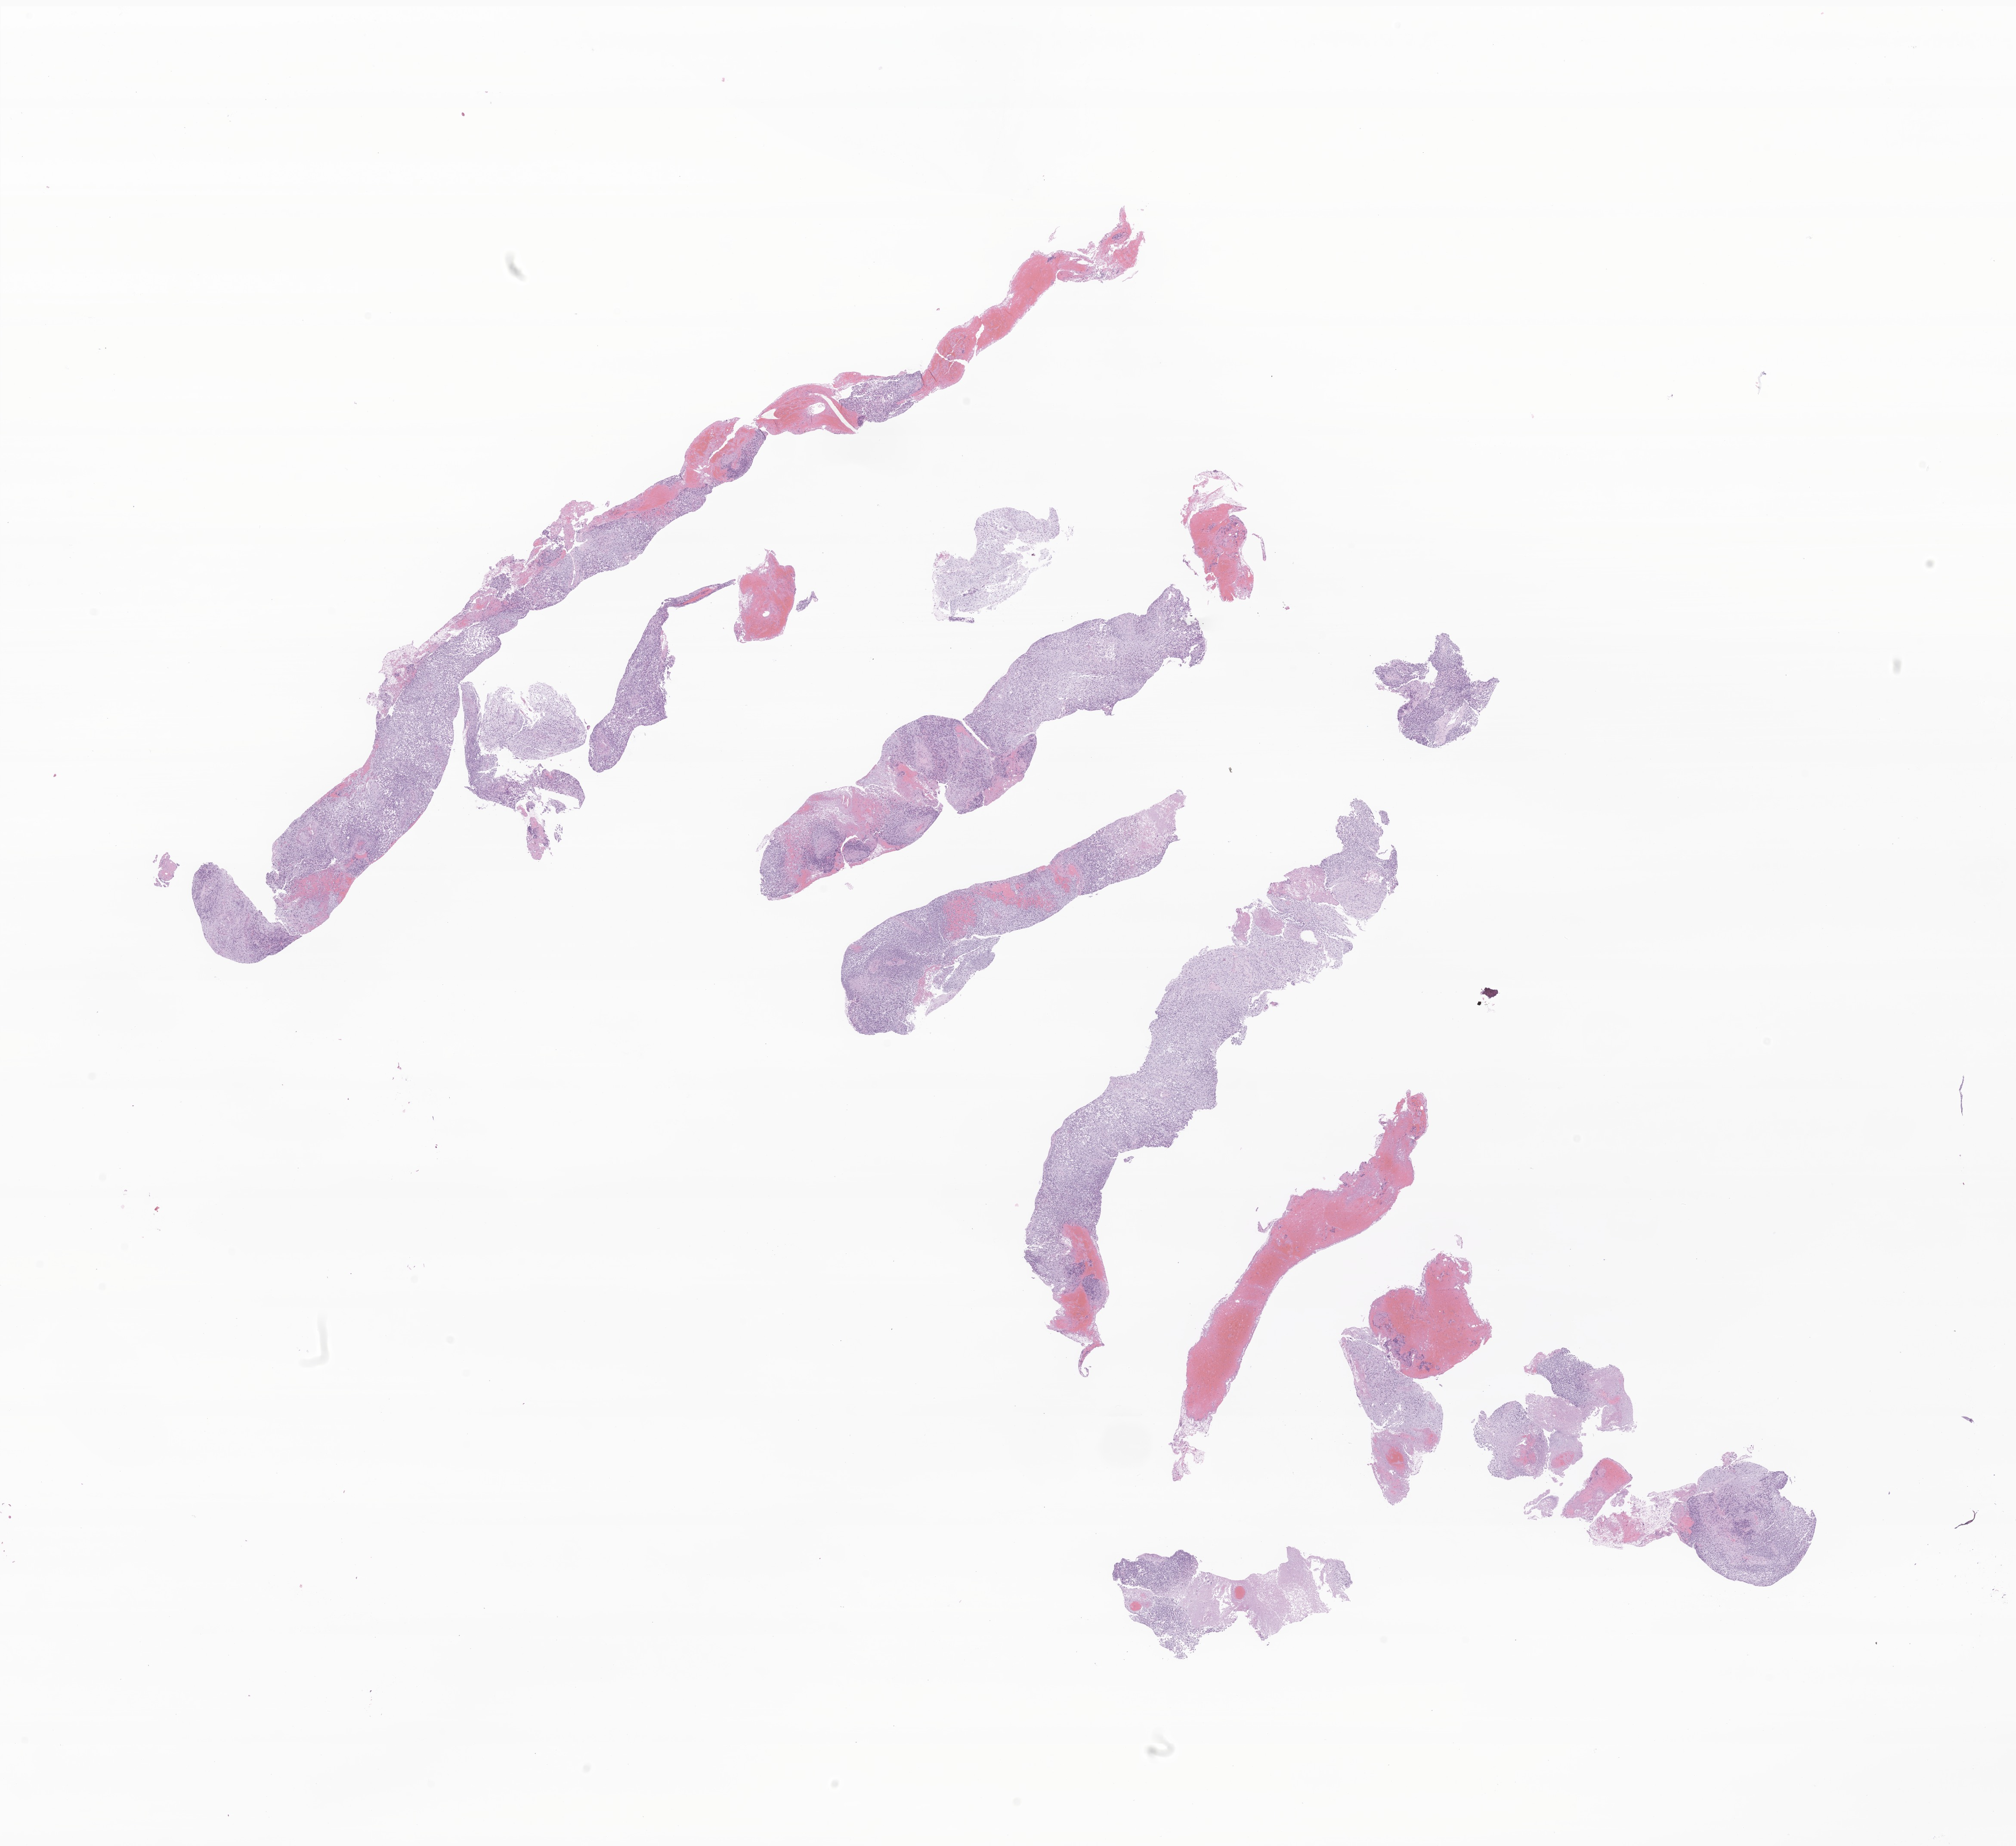
Whole-slide image, H&E stain of tumor tissue from the anterior mediastinum, low-resolution overview of the scanned area, about 19.7 x 18.1 mm, formalin-fixed, paraffin-embedded (FFPE) tissue. Patient: male, age 138 months.
Recorded diagnosis: Rhabdomyosarcoma, NOS.